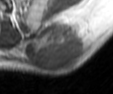
MRI of an extremity soft-tissue mass, one axial slice. Slice 25 of 42 in the series (ordered by position). MR volume resampled by the dataset authors to the PET/CT grid (not the native acquisition matrix). 3.27 mm slice thickness. 113 × 94 image matrix, field of view 110 × 92 mm. Male patient. From the clinical record (not read from this slice): histological type: leiomyosarcoma; grade: intermediate; site of the primary tumour: left pelvis.
Outlined on this slice (expert contour drawn on MRI and transferred to this co-registered scan by the dataset authors):
- gross tumour volume (mass): box from (x=24, y=18) to (x=89, y=72) px